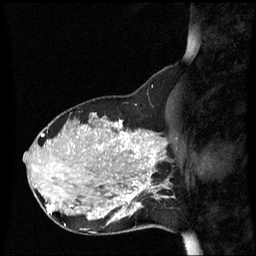
Breast MRI (dynamic contrast-enhanced), one sagittal slice. Position 22 of 60 along the scan axis. Dynamic contrast-enhanced series, image 2 of 3 at this slice position (ordered by acquisition). 1.5 T. TE 4.2 ms, TR 8.9 ms. 256 × 256 image matrix, field of view 220 × 220 mm. Female patient, age 31 years. From the clinical record (not read from this slice): setting: breast cancer imaged before/during neoadjuvant chemotherapy; receptor status: HR-positive, HER2-negative.
Annotated regions visible in this slice (semi-automatically segmented with operator editing):
- analysis volume of interest (the breast-tissue region the enhancement analysis was run in; not a lesion): bounding box <90,180,152,235> (left, top, right, bottom; pixels)
- tumour enhancement mask (voxels above the 70 % enhancement threshold inside the analysis volume of interest): <127,180,151,207>